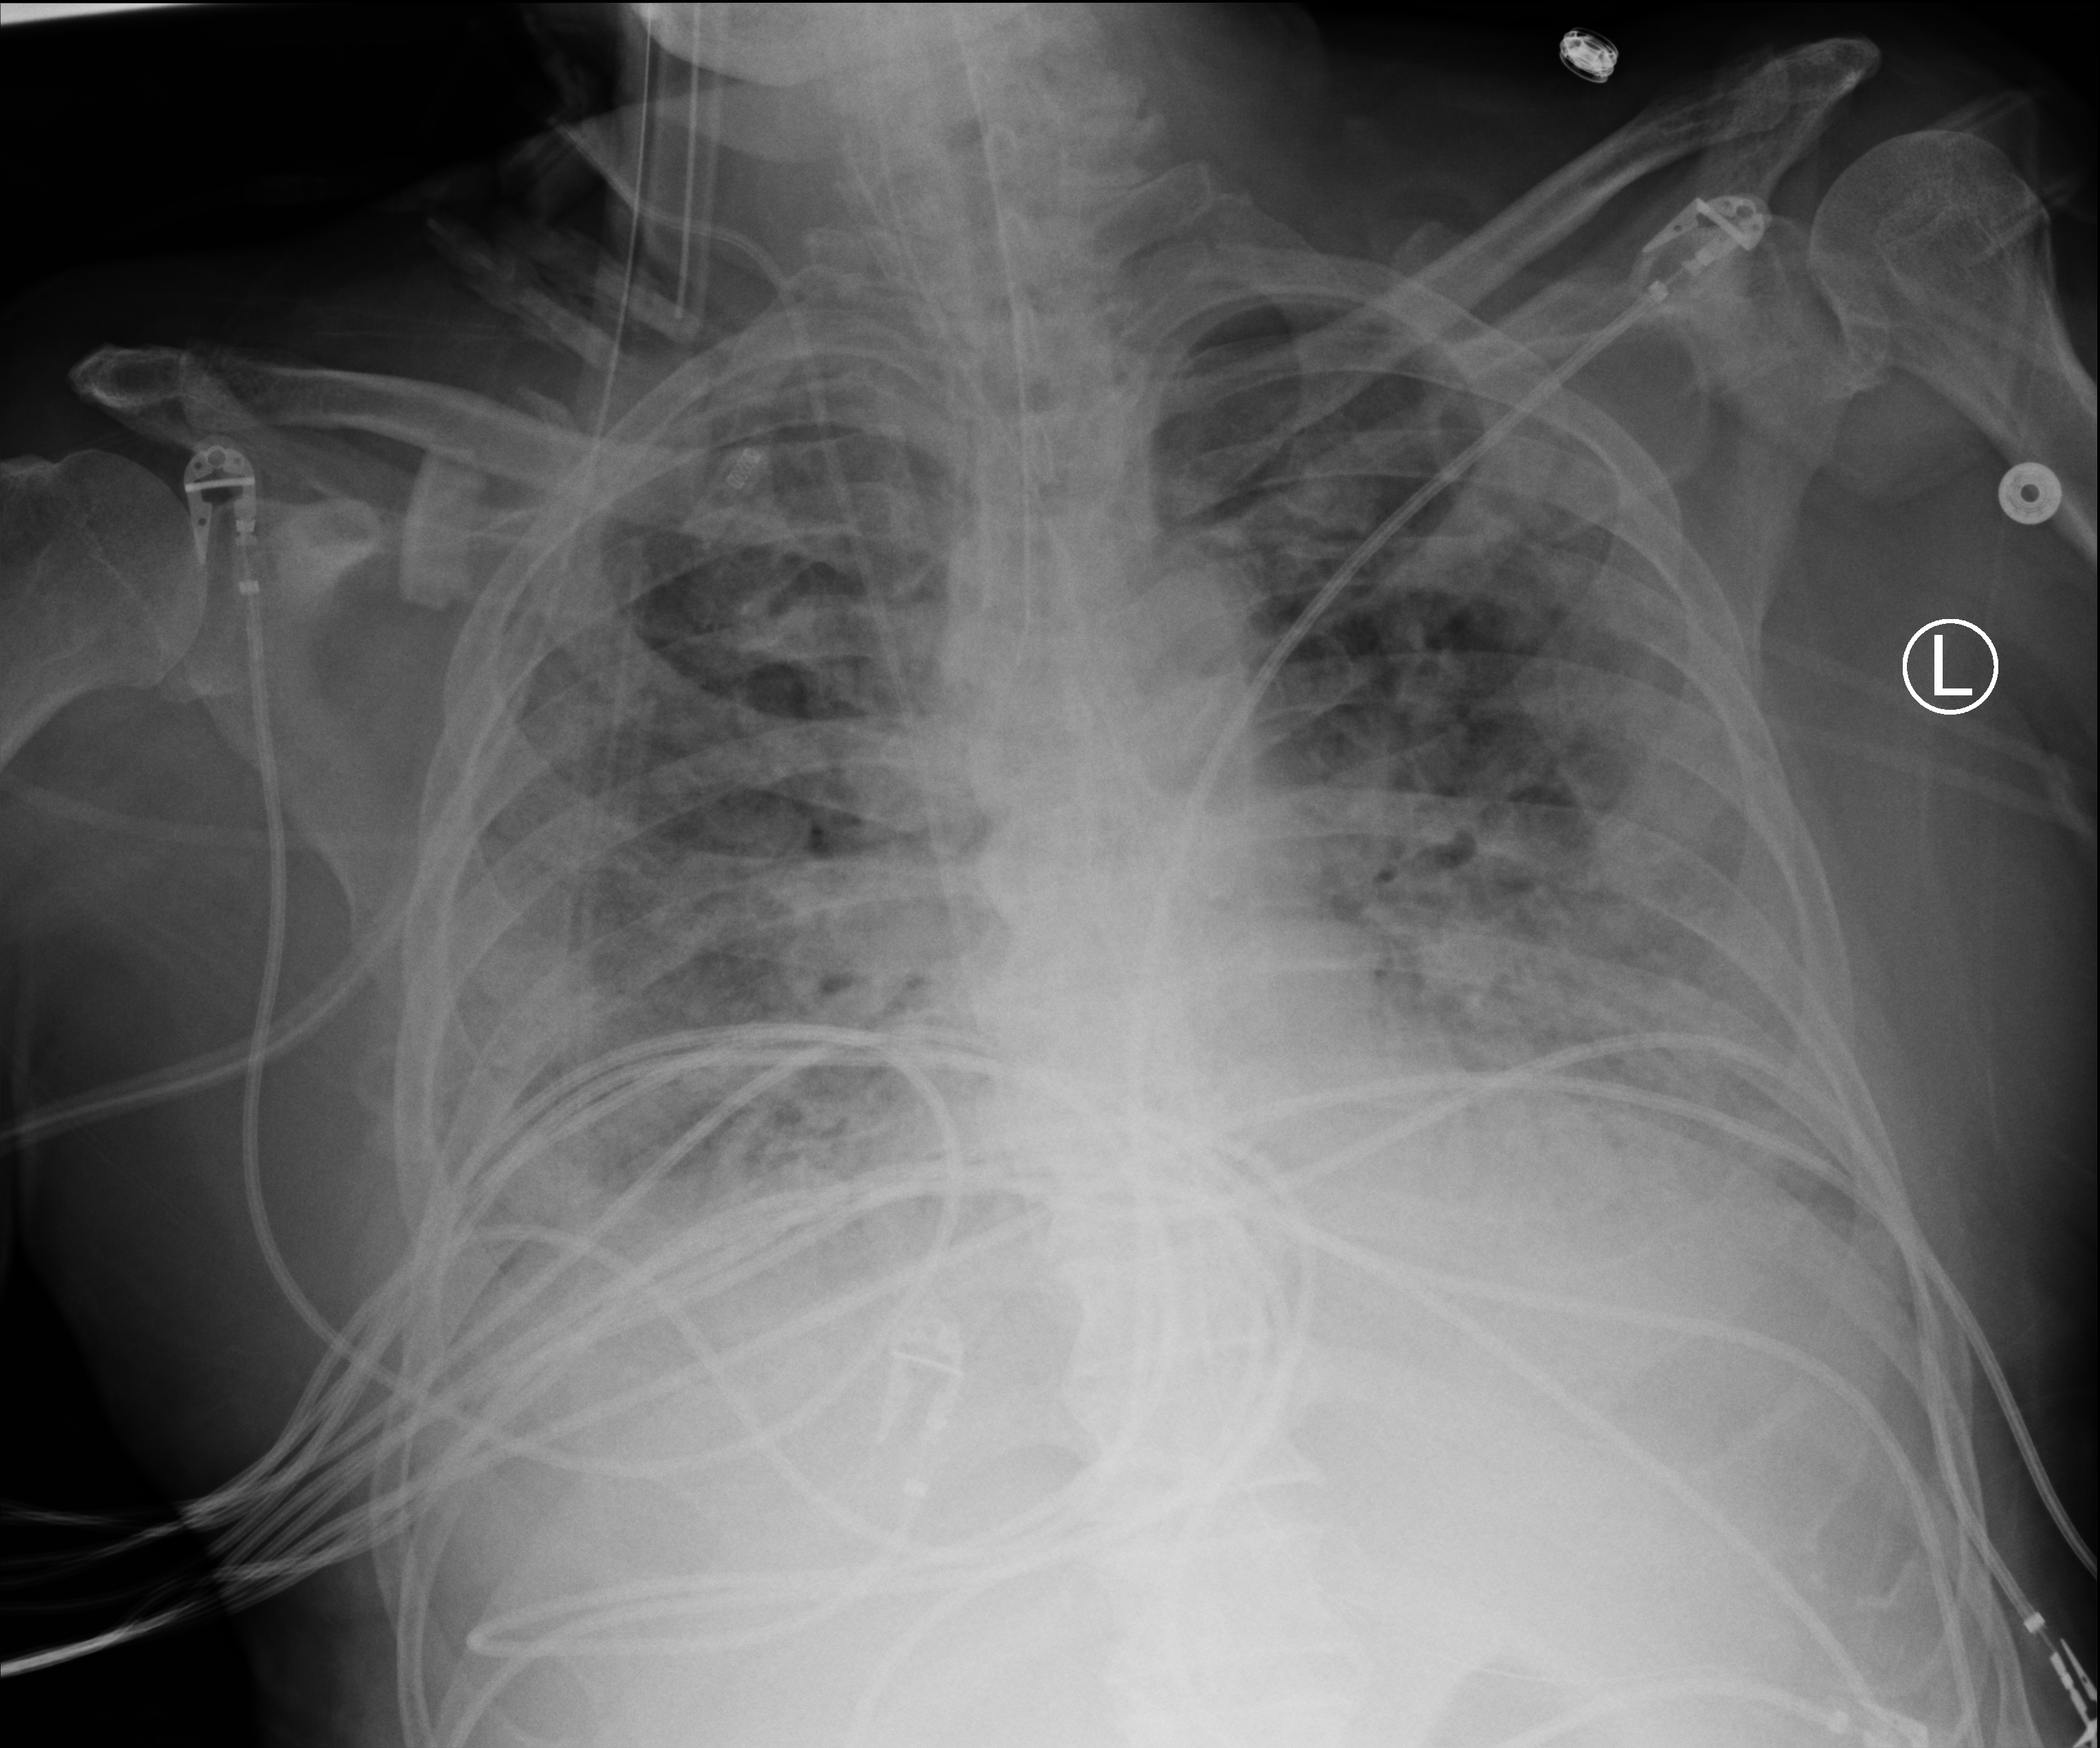
Portable chest radiograph. Male patient hospitalised with COVID-19, age 75–90 years.
Admission-level facts for this patient (not findings on this image; timing relative to this image not recorded):
- admitted to intensive care during this hospital stay: yes
- hypertension (admission record): yes